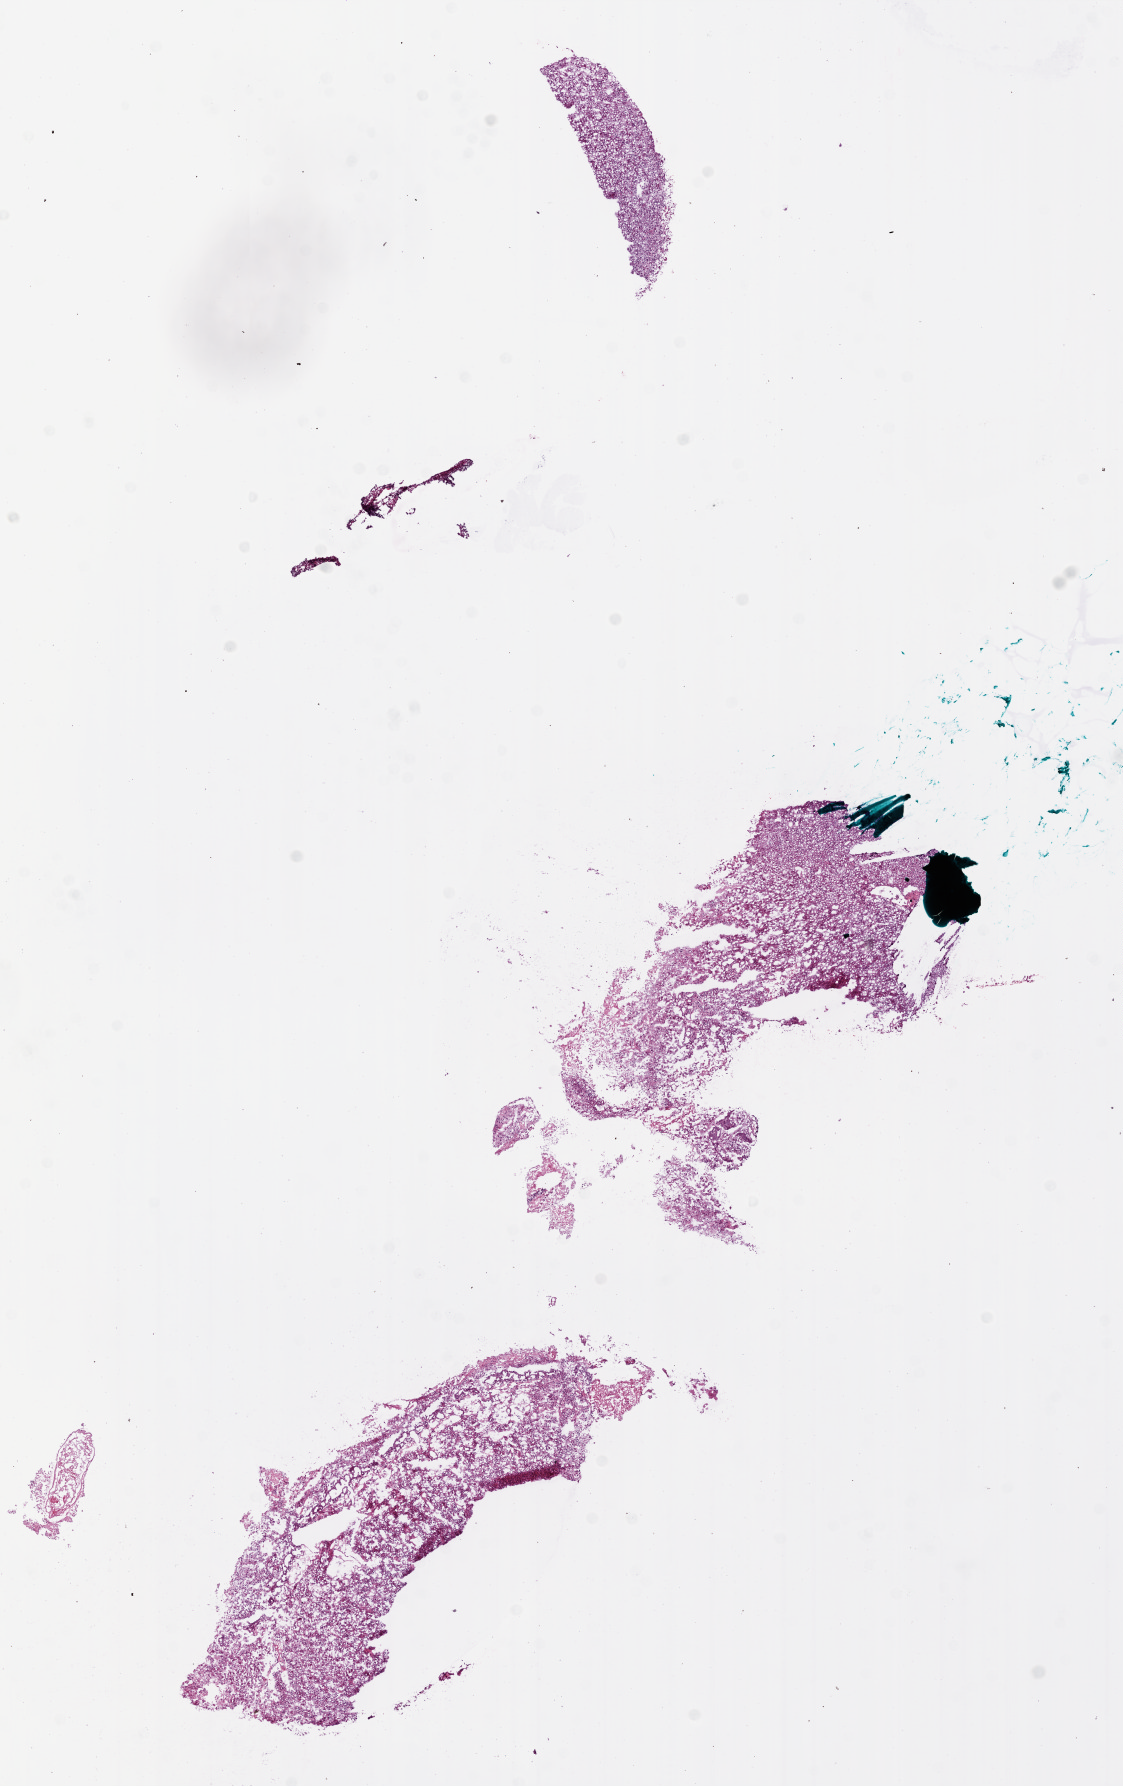
Whole-slide histology image, H&E — shown as a low-resolution overview of the whole scanned area (about 9.0 x 14.3 mm, slide scanned at 20x); frozen section from the bottom of the tissue portion; primary tumour sample from the brain. Male, age 57 years at initial diagnosis. Slide review estimates, as recorded: tumour cells 95%, tumour nuclei 100%, normal cells 0%, stromal cells 0%, necrosis 5%. Infiltration values recorded for this section: lymphocyte infiltration 0%.
Diagnosis: Glioblastoma.